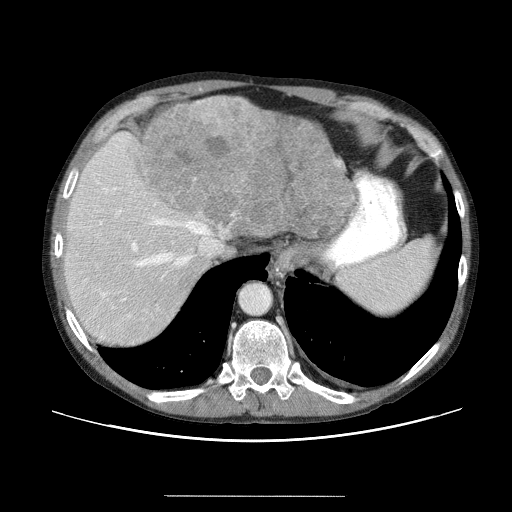
Contrast-enhanced abdominal CT (liver protocol), one axial slice. Slice 48 of 69 in the series (ordered by position). 120 kVp. Soft-tissue window (W 400 / L 40 HU). 512 × 512 image matrix. Case-level facts recorded for this patient, not image findings: diagnosis: hepatocellular carcinoma (patient treated with transarterial chemoembolisation; whether this scan precedes or follows treatment is not stated here); TNM stage (as recorded): Stage-IVB; Child-Pugh class: B; tumour differentiation: poorly differentiated.
Structures marked on this image (semi-automatic segmentation, software-assisted and operator-edited):
- liver parenchyma outside the tumour (the mass and vessels are separate outlines, so this box may not span the whole liver): bounding box [x1, y1, x2, y2] px = [62, 96, 346, 352]
- mass: [141, 96, 359, 249]
- liver vessels: [99, 190, 221, 320]